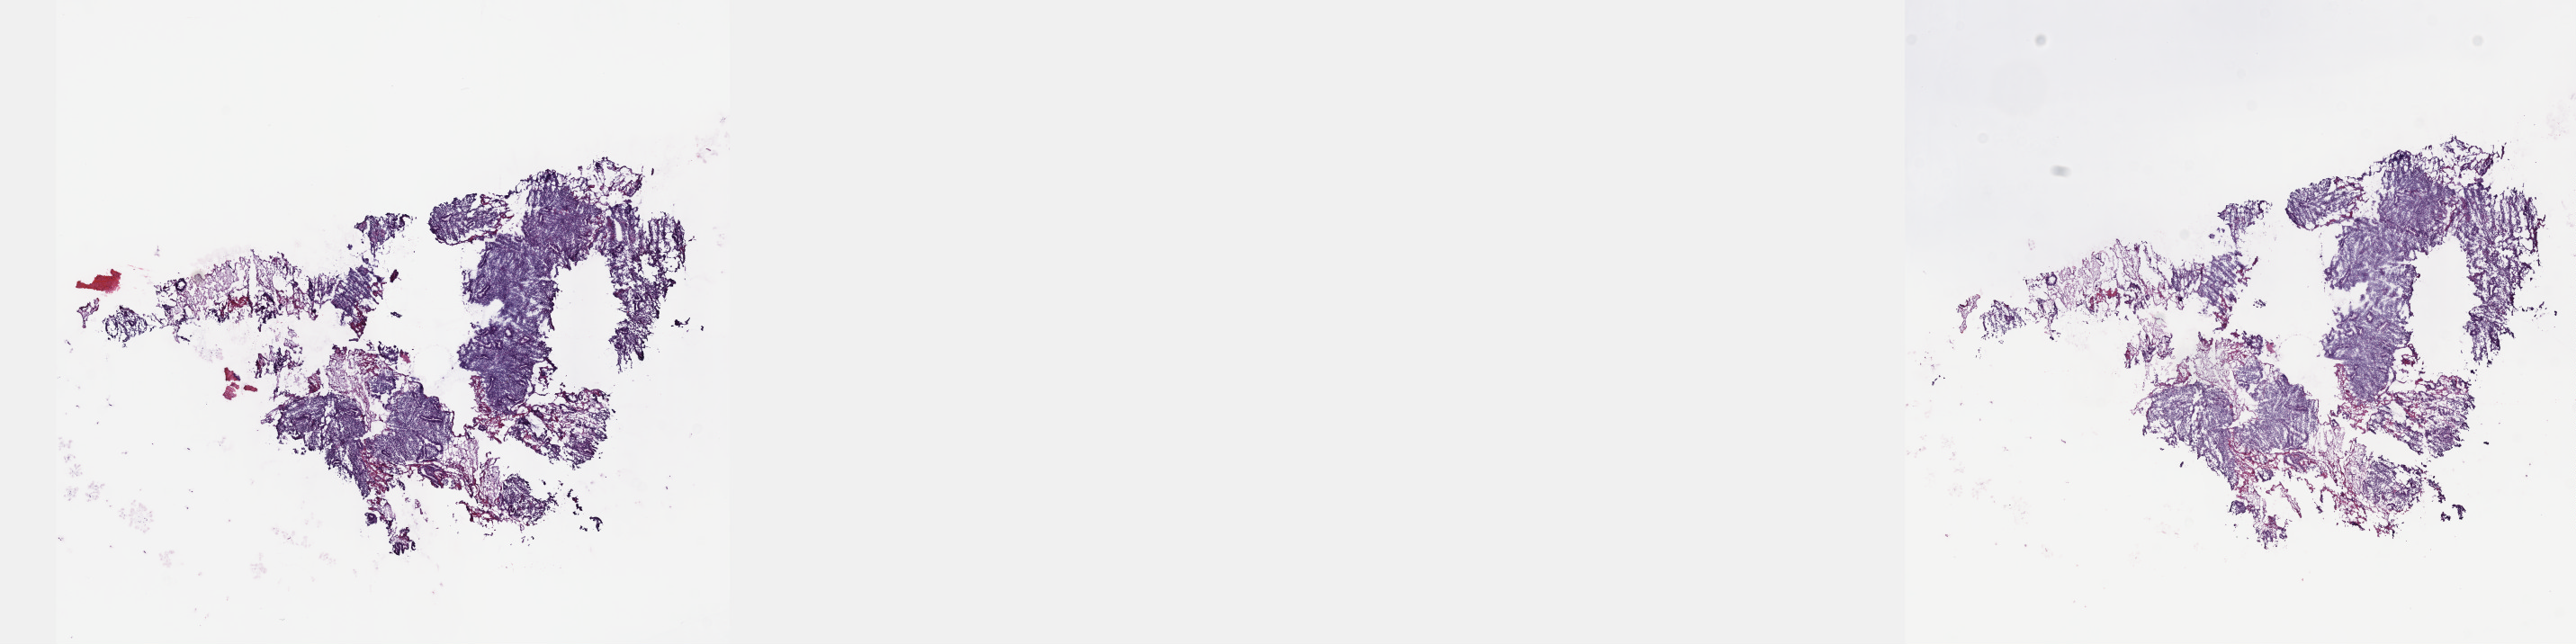
Hematoxylin and eosin (H&E) stained whole-slide image, whole scanned area (about 23.1 x 5.8 mm, slide scanned at 40x) shown as a low-resolution overview; frozen section; cervix, primary tumour sample. Female, age 36 years at initial diagnosis. Histologic grade: G3 (poorly differentiated). Composition of this section per pathologist review: tumour cells 75%, tumour nuclei 75%, normal cells 10%, stromal cells 15%, necrosis 0%. Inflammatory infiltration, as recorded: lymphocyte infiltration 5%, monocyte infiltration 1%, neutrophil infiltration 1%.
- pathologic diagnosis: Squamous cell carcinoma, NOS (cervix uteri)
- FIGO stage: IB1